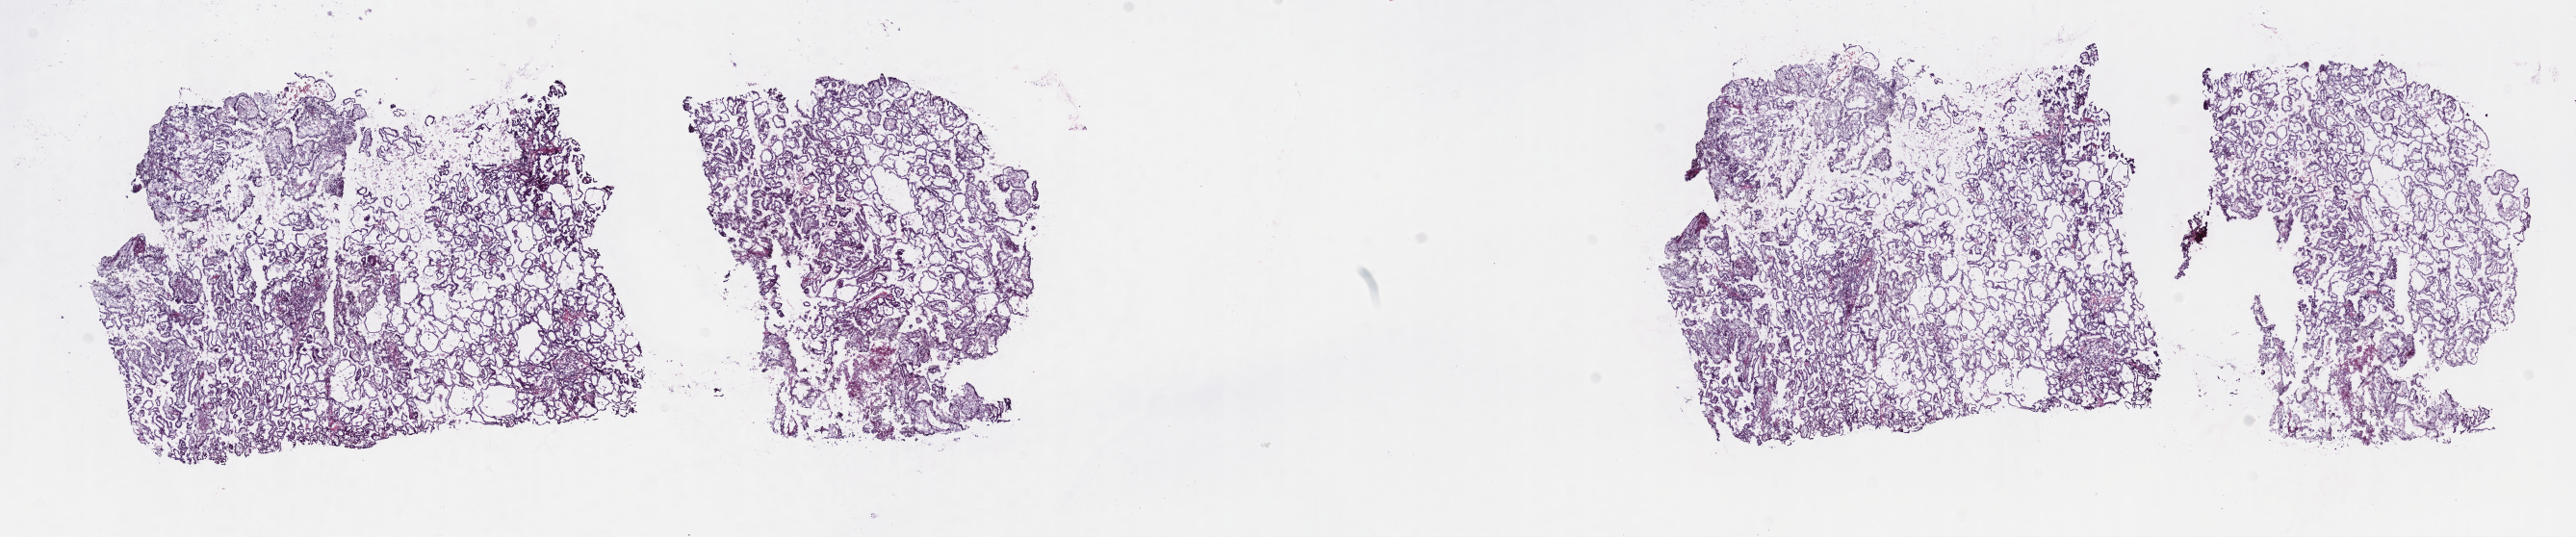
Whole-slide histology image, Hematoxylin and eosin (H&E) stained — a low-resolution overview of the entire scanned area, about 21.6 x 4.5 mm. Frozen section from the top of the tissue portion. Kidney, primary tumour sample. Male patient; age at initial diagnosis 60 years. Slide review estimates, as recorded: tumour cells 80%, tumour nuclei 94%, normal cells 0%, stromal cells 5%, necrosis 15%. Infiltration values recorded for this section: lymphocyte infiltration 2%, monocyte infiltration 3%, neutrophil infiltration 0%.
AJCC pathologic stage: I (6th edition). Histologic diagnosis: Papillary adenocarcinoma, NOS.